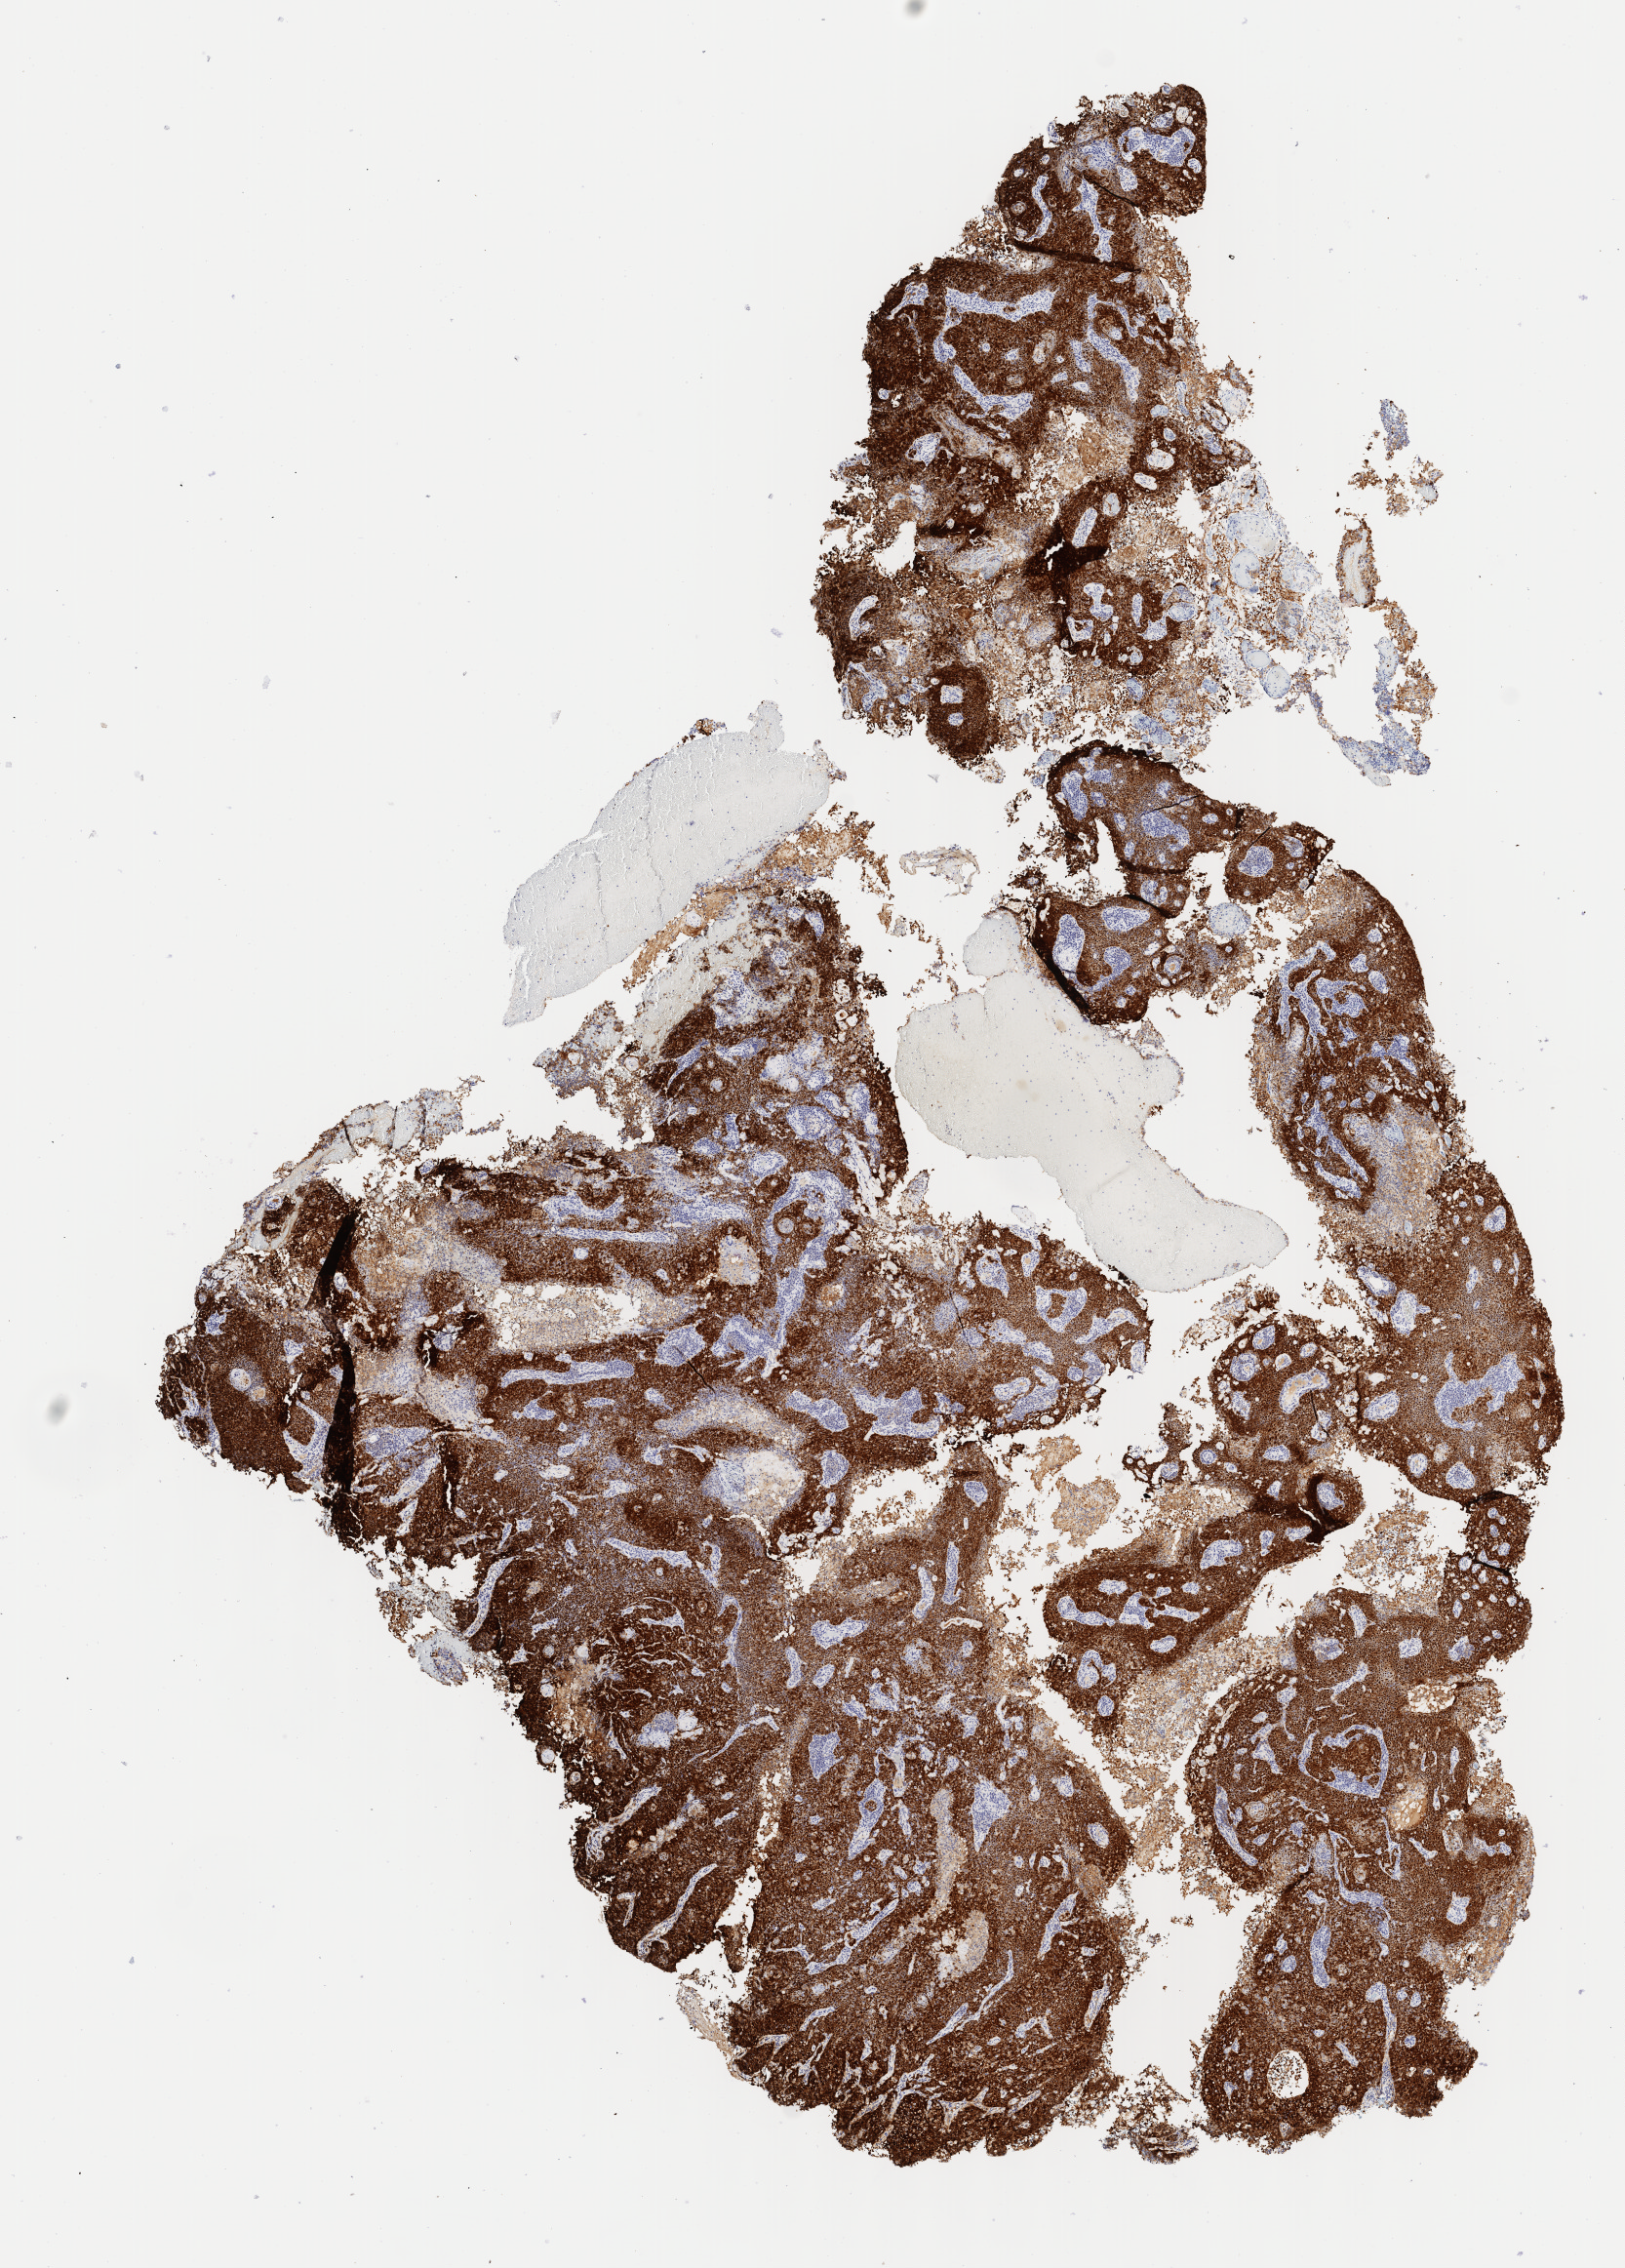
Whole-slide image, immunohistochemical stain for p16 (p16INK4a) — low-resolution overview of the scanned area, about 6.6 x 9.2 mm. Specimen: tumor tissue. Site: cervix. Patient: female, 45 years old.
* diagnosis: Squamous cell carcinoma, keratinizing, NOS